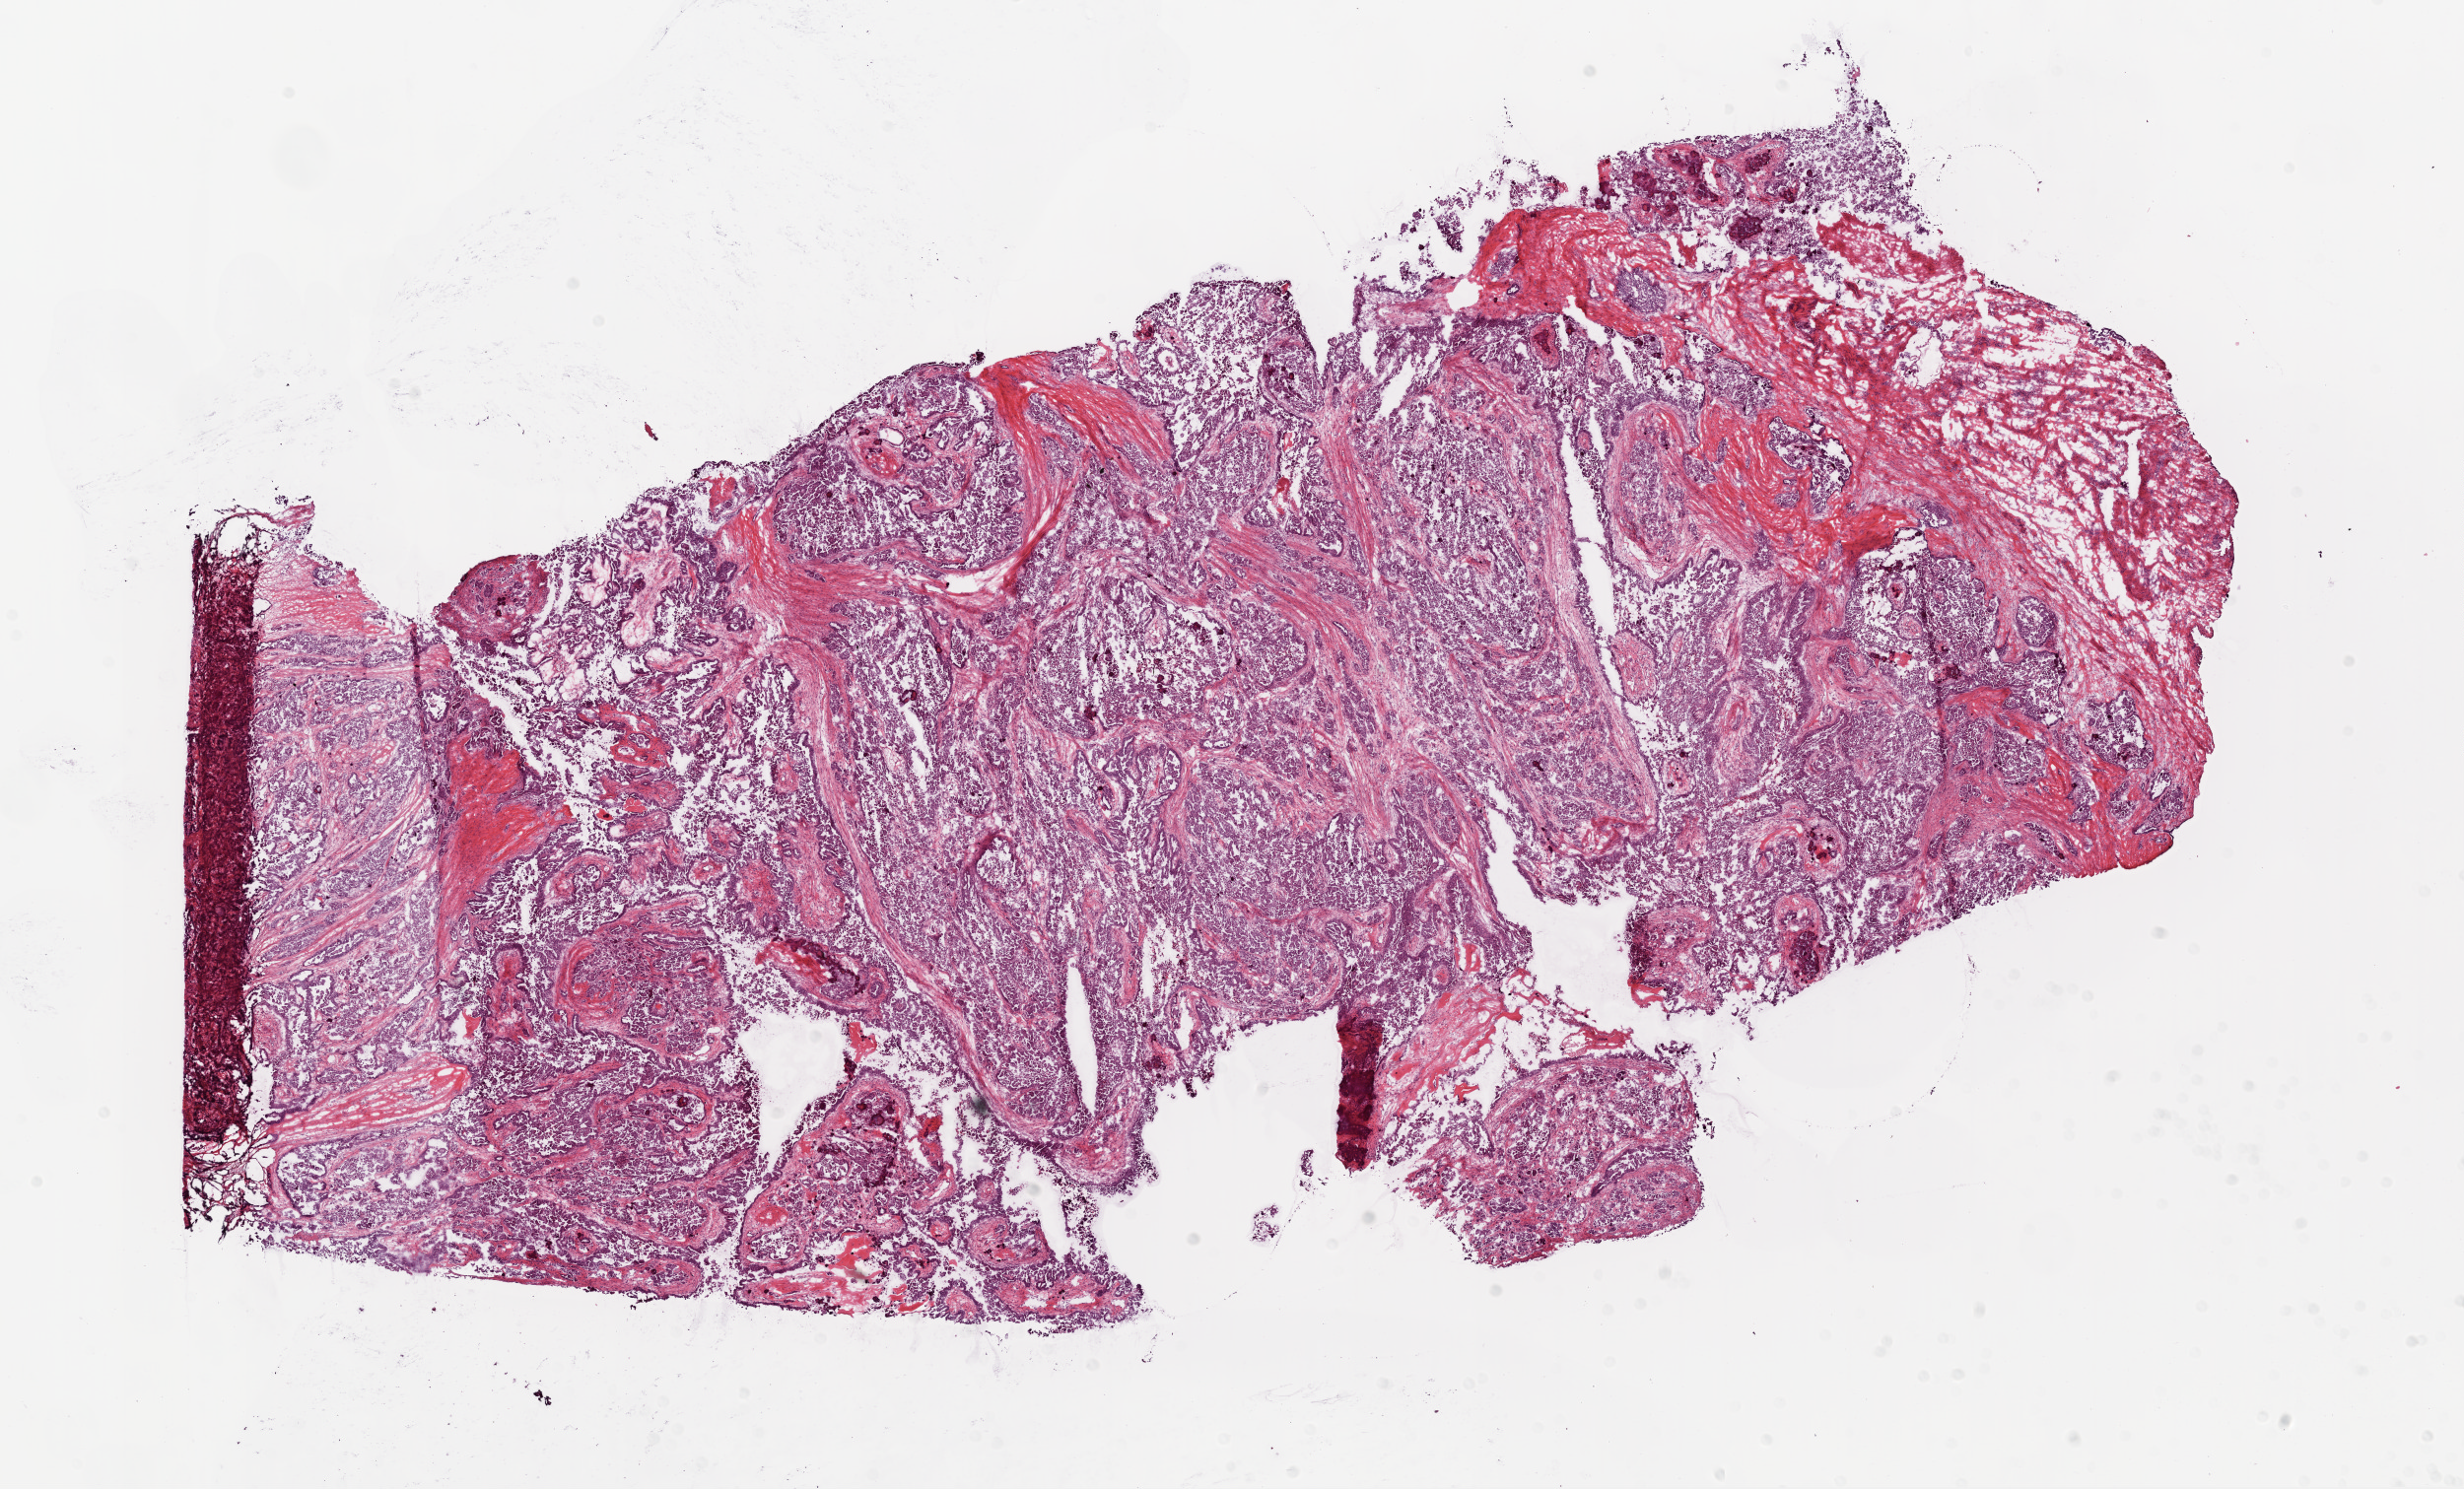
H&E whole-slide image — shown as a low-resolution overview of the whole scanned area (about 20.1 x 12.1 mm); frozen section from the bottom of the tissue portion; primary tumour sample from the ovary. Patient: female, age at initial diagnosis 55 years. Histologic grade: G2 (moderately differentiated). Pathologist review of this section (percent, as recorded): tumour cells 90%, tumour nuclei 90%, normal cells 0%, stromal cells 10%, necrosis 0%.
Pathologic diagnosis: Serous cystadenocarcinoma, NOS. FIGO stage: IIIC.